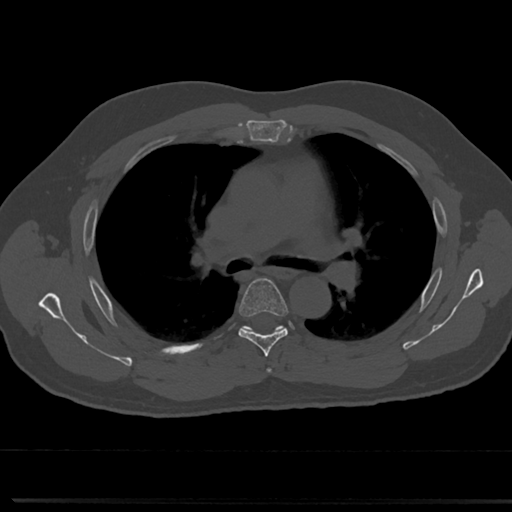
CT including the spine, one axial slice; reconstruction kernel Br40s/3; bone window (W 1800 / L 400 HU); 0.5 mm slice thickness; 512 × 512 image matrix, field of view 355 × 355 mm. Patient: male, 61 years. Case-level facts recorded for this patient, not image findings: primary cancer: prostate.
Annotated regions visible in this slice (semi-automatic segmentation, software-assisted and operator-edited):
- T4 vertebra: bounding box [x1, y1, x2, y2] px = [264, 361, 273, 374]
- T5 vertebra: [219, 278, 300, 348]